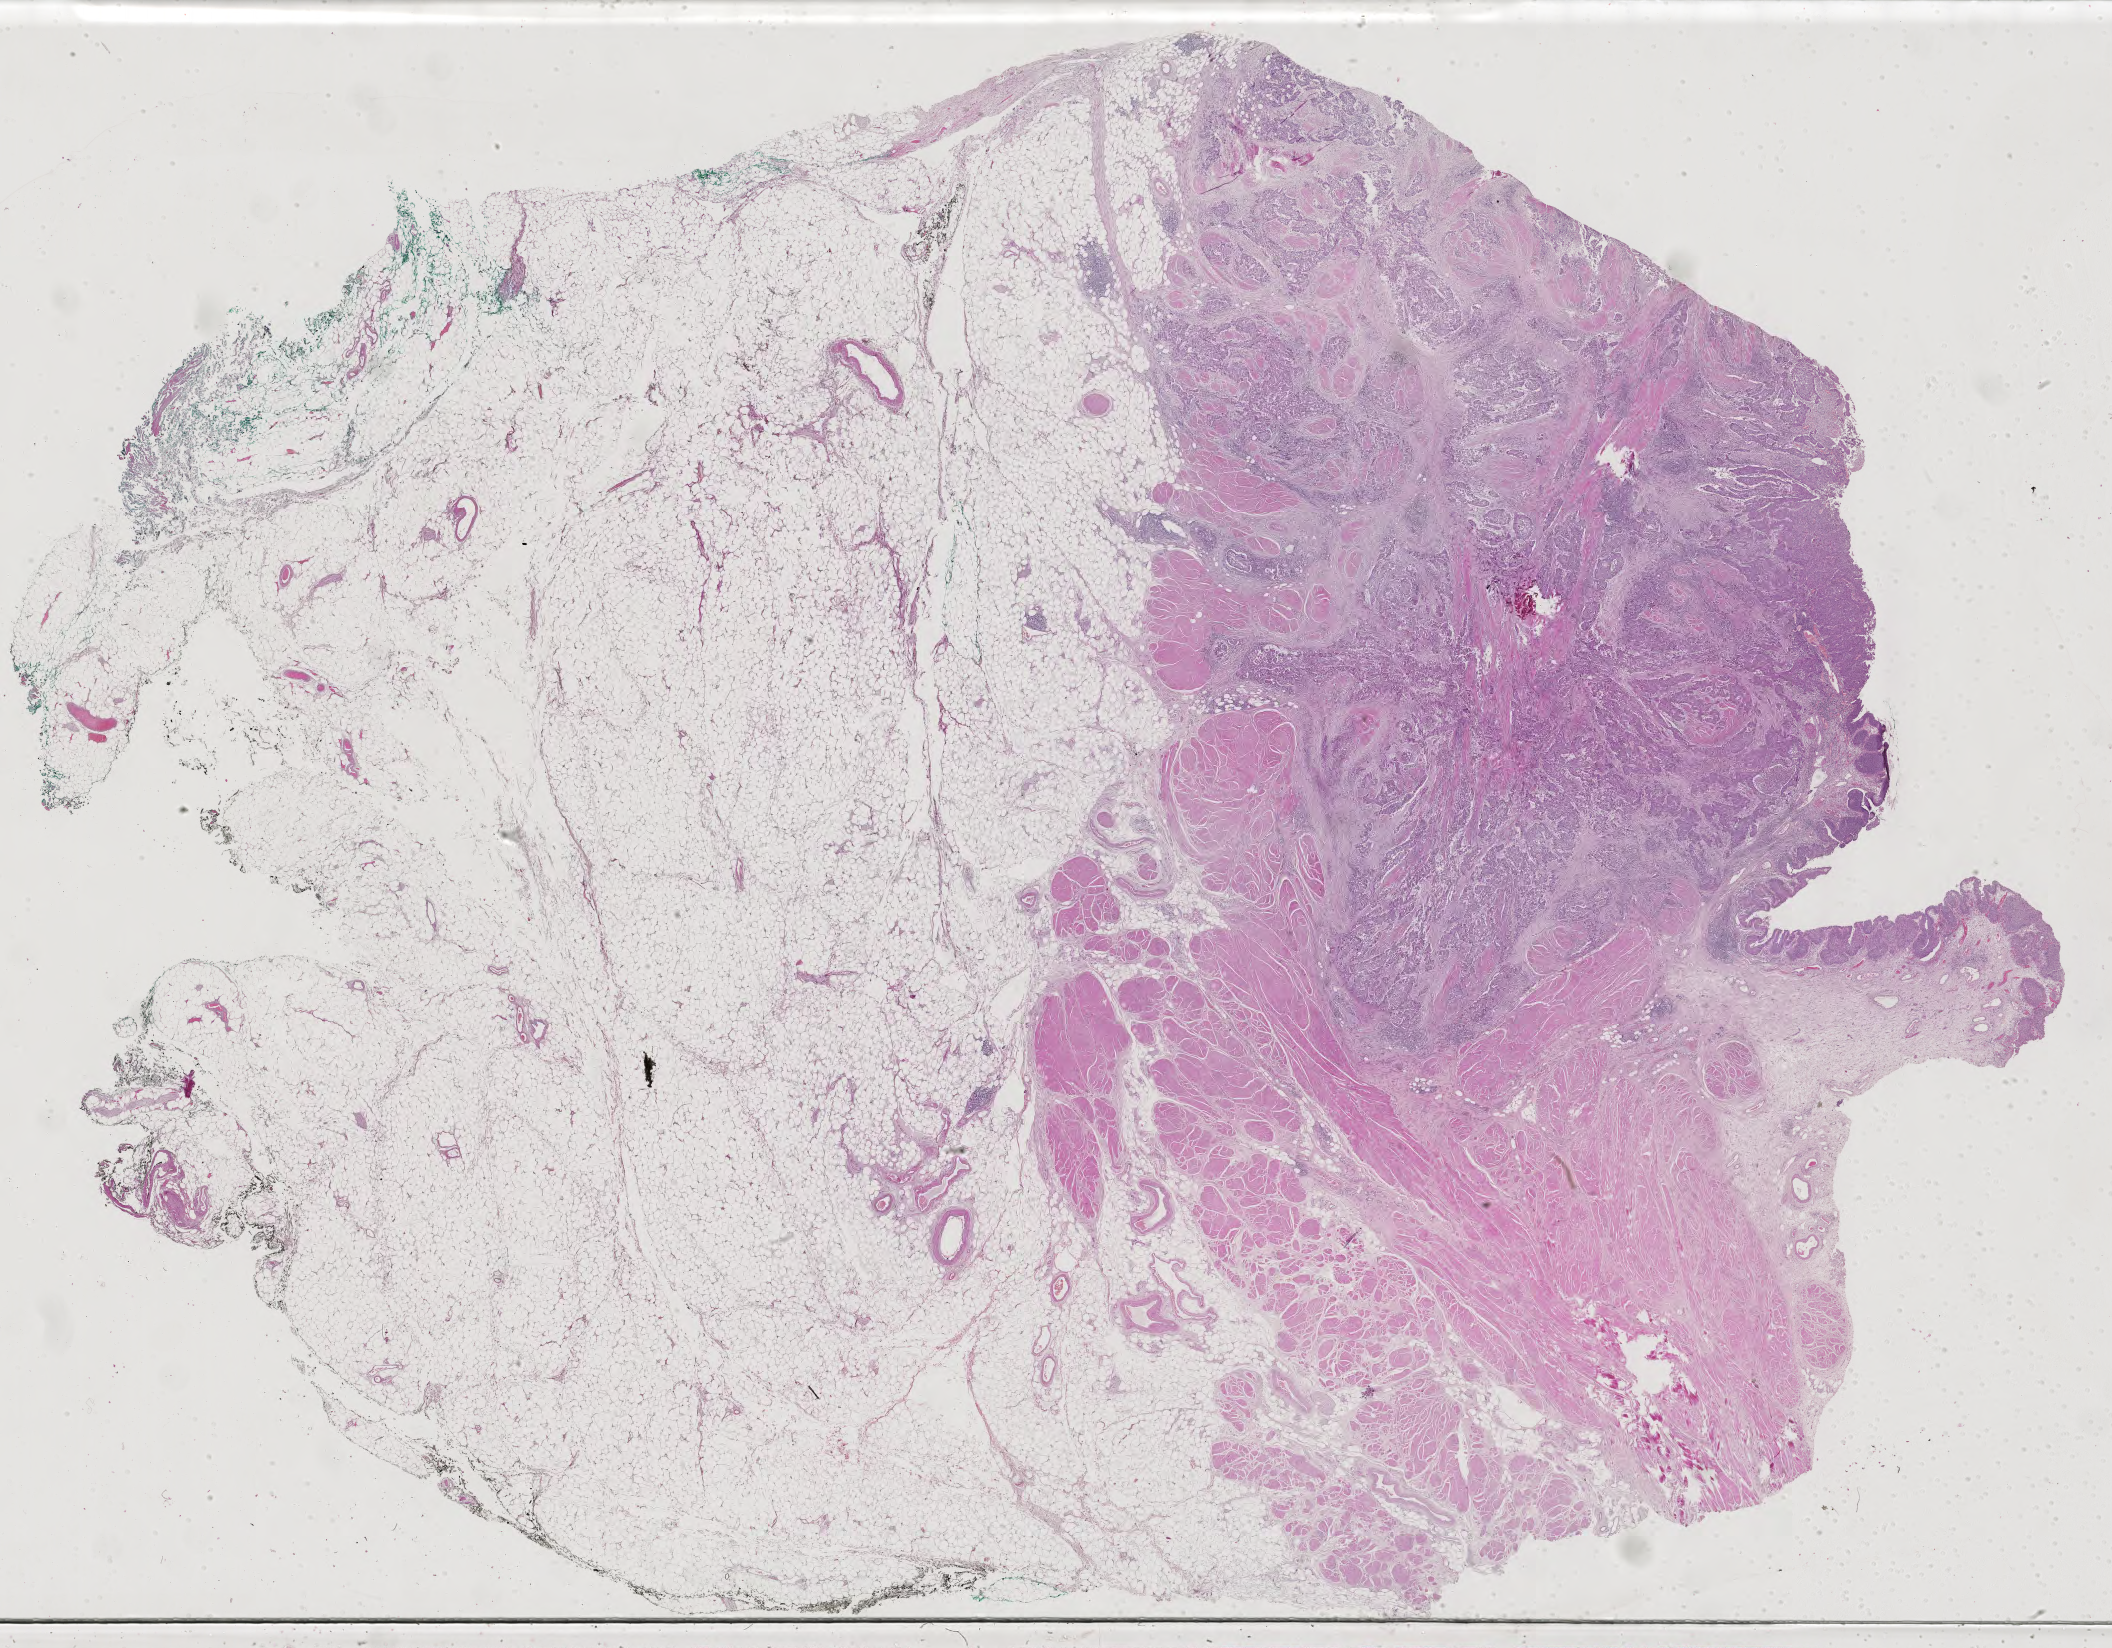
H&E whole-slide image — whole scanned area (about 30.8 x 24.0 mm) shown as a low-resolution overview, formalin-fixed paraffin-embedded (FFPE) diagnostic section, bladder, primary tumour sample. Male patient; age at initial diagnosis 63 years. Histologic grade: high grade.
AJCC pathologic stage: IV. Pathologic diagnosis: Transitional cell carcinoma (posterior wall of bladder).